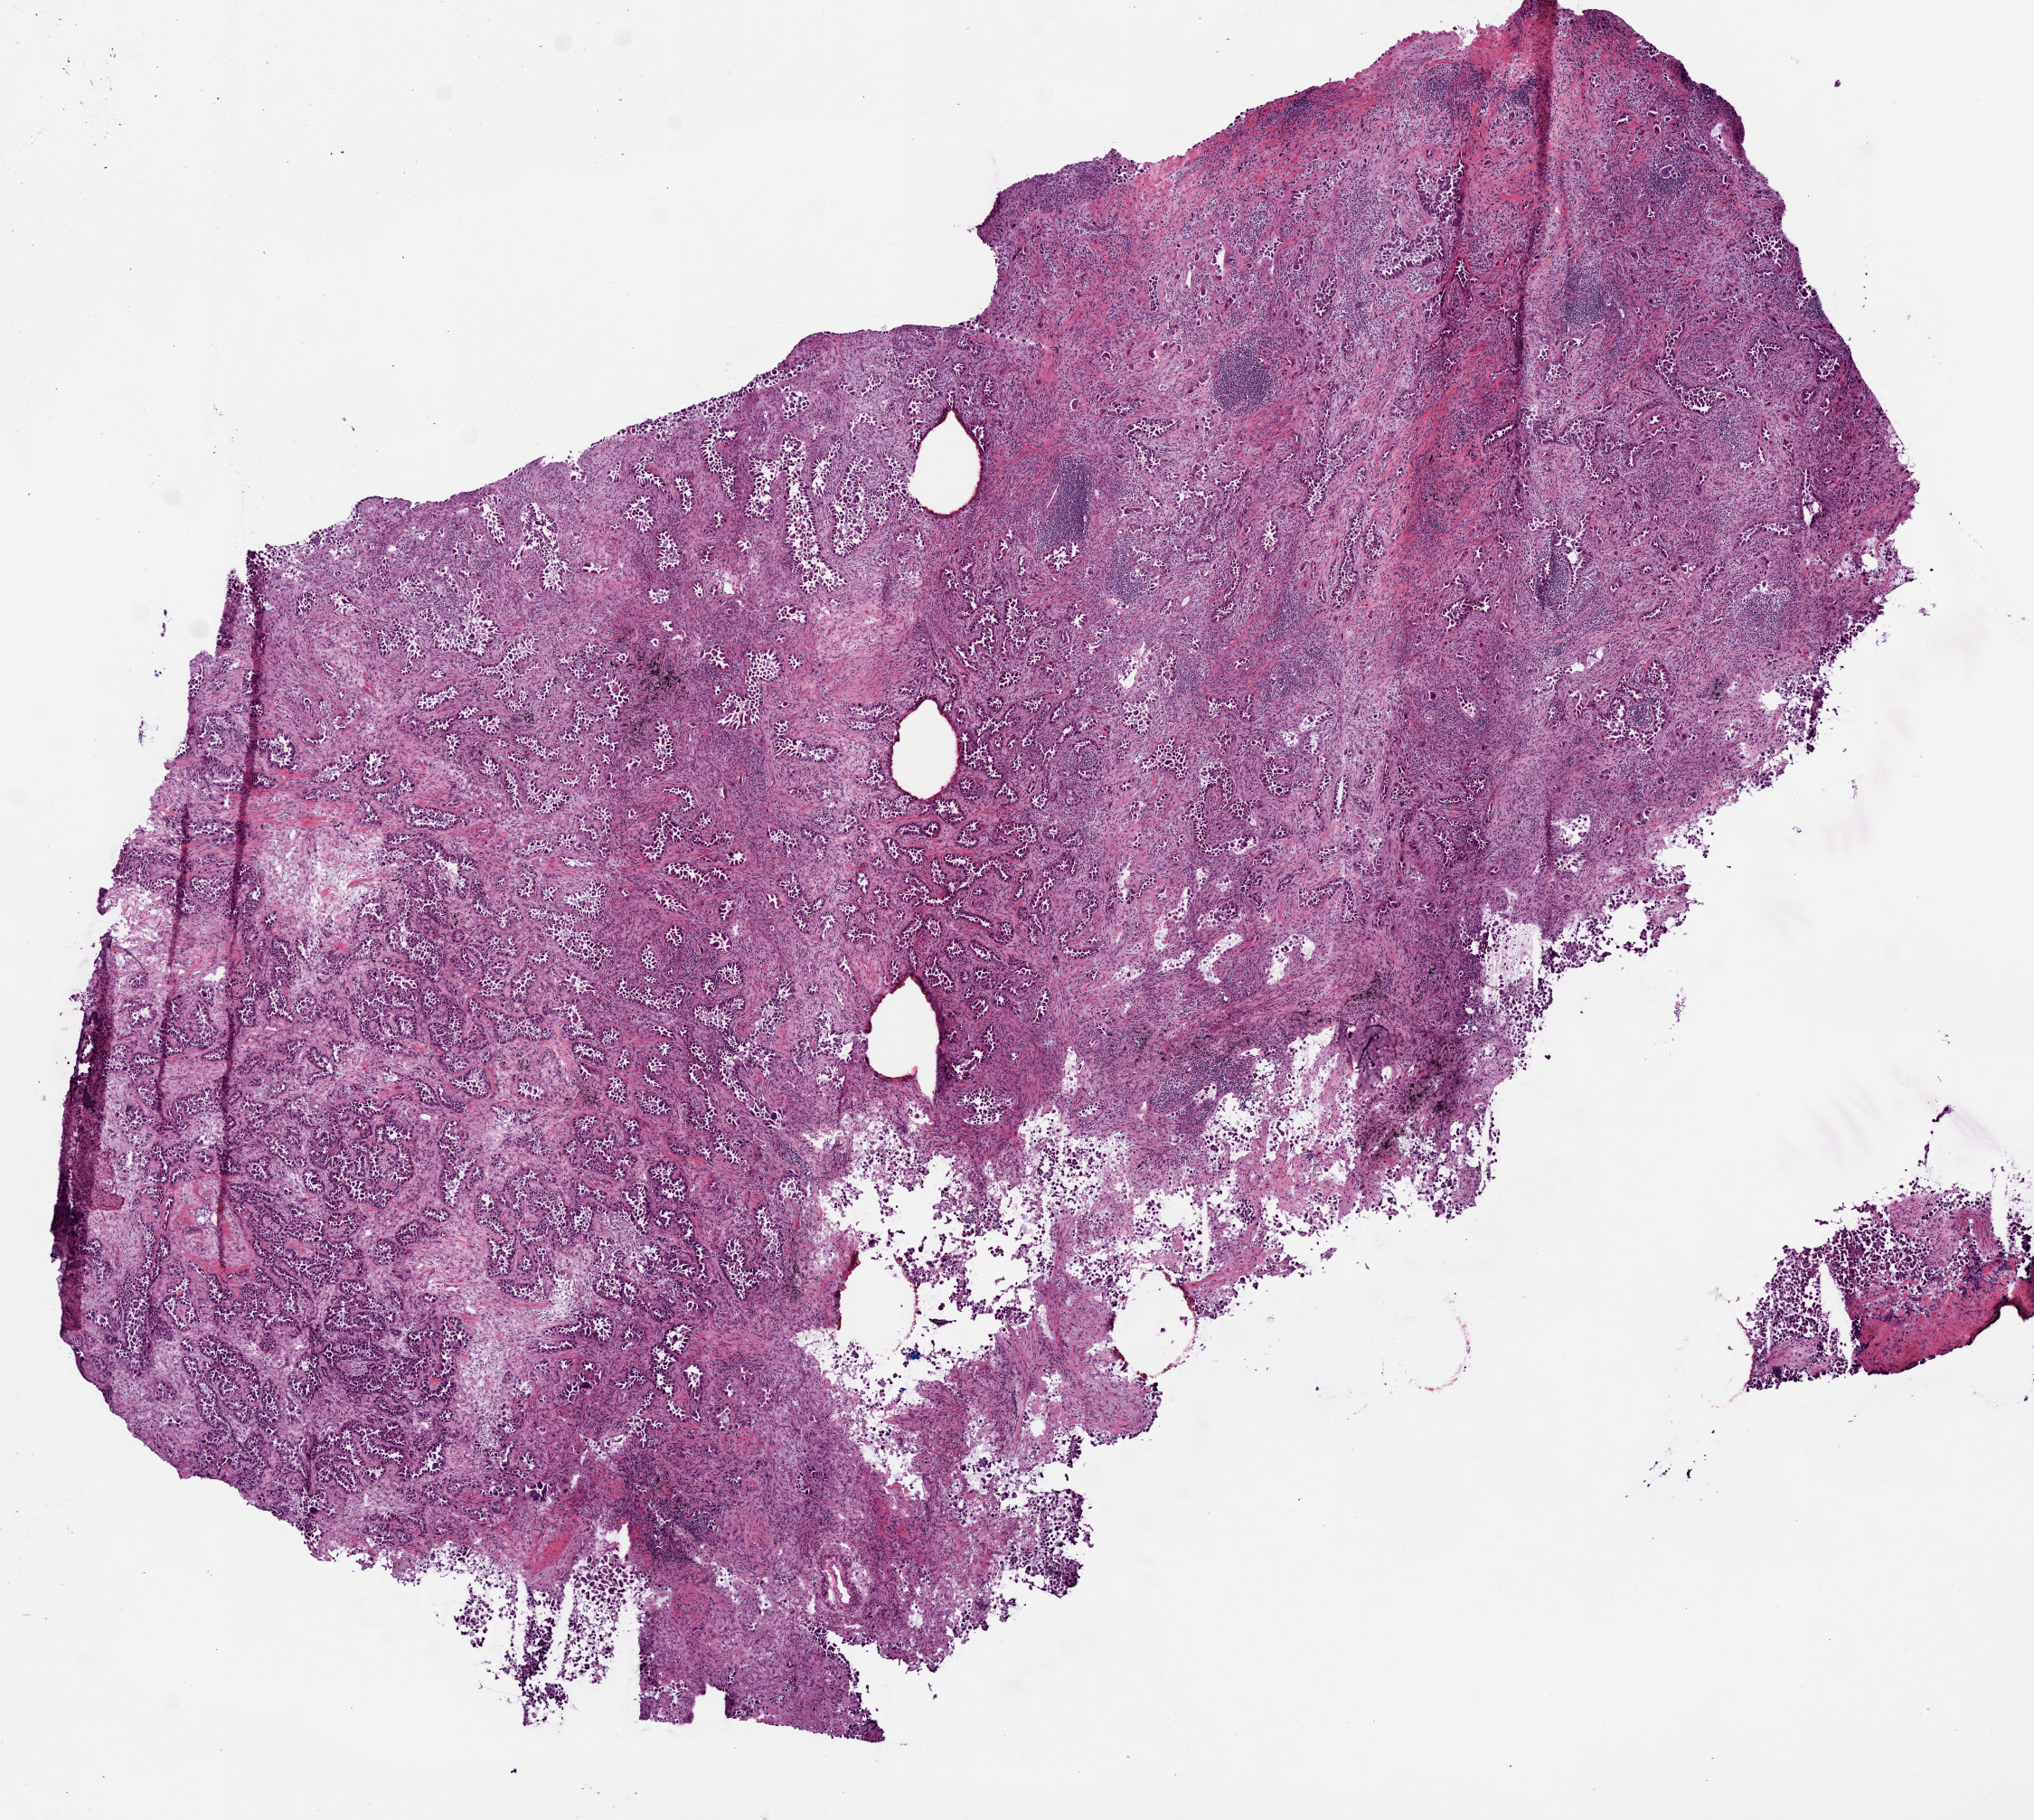
Digitized H&E-stained tissue section (whole slide) — low-resolution overview of the scanned area, about 9.0 x 8.1 mm; frozen section from the top of the tissue portion; sample: primary tumour, lung. Patient: male, age at initial diagnosis 65 years. Pathologist review of this section (percent, as recorded): tumour cells 100%, tumour nuclei 71%, normal cells 0%, stromal cells 0%, necrosis 0%. Inflammatory infiltration, as recorded: lymphocyte infiltration 5%, monocyte infiltration 0%, neutrophil infiltration 0%.
Histologic diagnosis: Invasive micropapillary carcinoma (upper lobe, lung). Laterality: left. AJCC pathologic stage: IB.